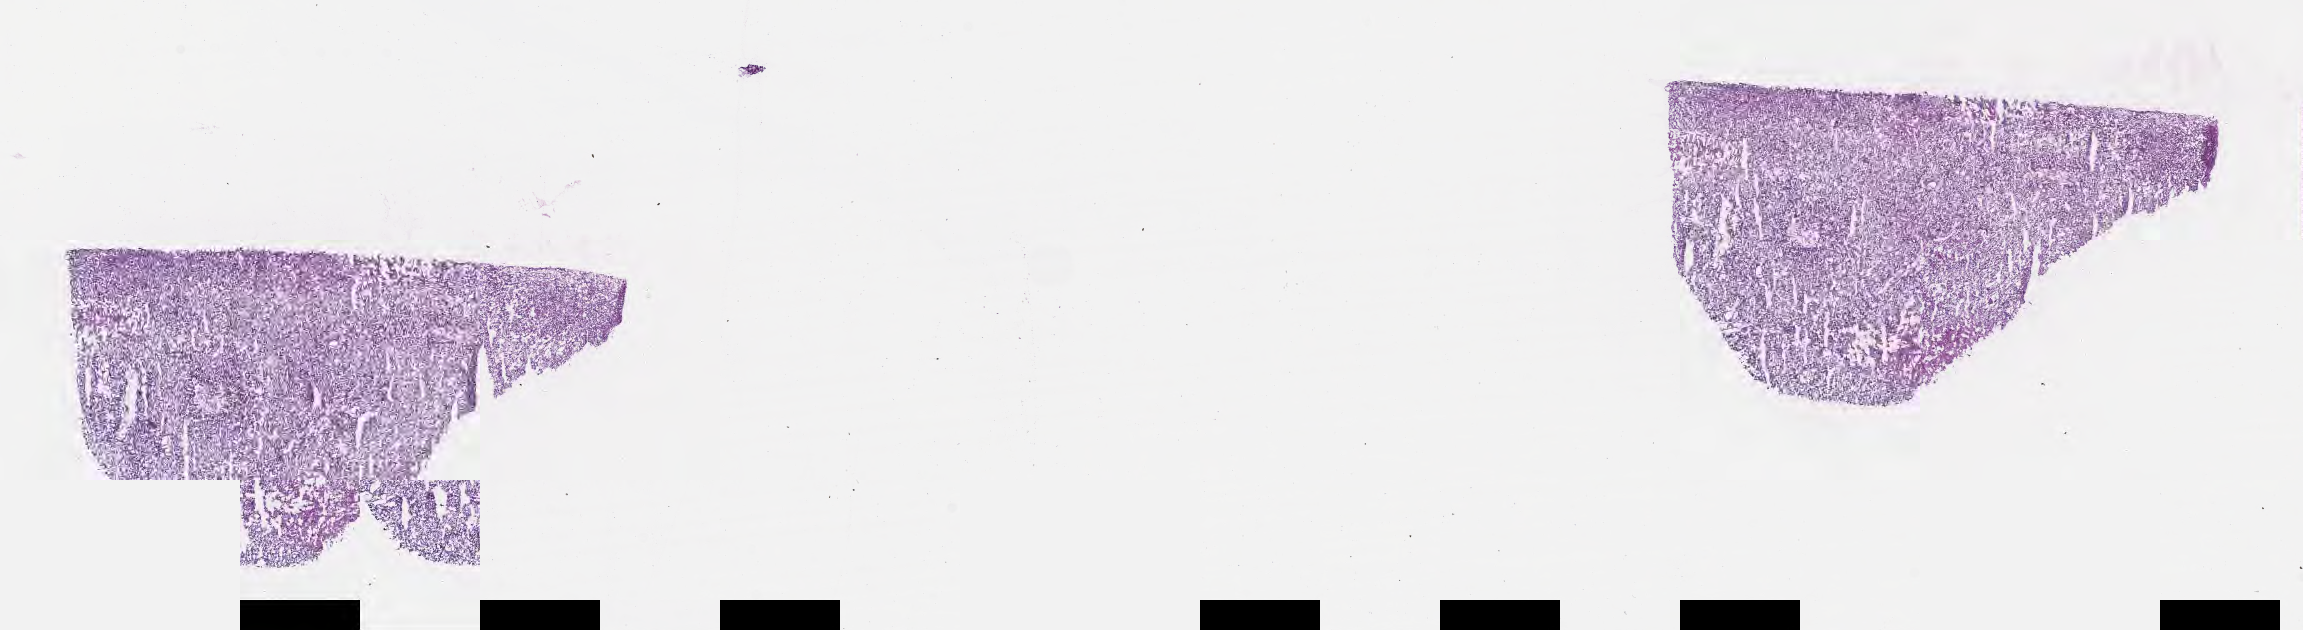
Haematoxylin and eosin whole-slide image, shown as a low-resolution overview of the whole scanned area (about 18.6 x 5.1 mm); frozen section; specimen: metastatic tumor tissue, resected from brain. Patient: female, age at initial diagnosis 65 years.
Patient diagnosis (primary): Carcinoma, NOS.